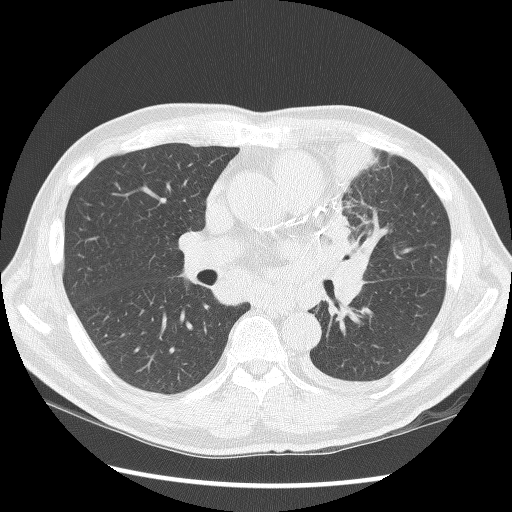
Axial slice from a low-dose chest CT screening exam; second annual screen; lung window (W 1500 / L -600 HU); 2.5 mm slice thickness; lung (sharp) reconstruction kernel (BONE); 120 kVp; slice 59 of 136 in the series; 512 × 512 image matrix. Male, age 64 years at enrolment. Former smoker at enrolment.
- Expert-annotated lung lesion, bounding box [x1, y1, x2, y2] px = [306, 130, 394, 278].
- No non-calcified nodule or mass ≥4 mm was recorded by the screening reader at this exam.
- Participant outcome: lung cancer diagnosed 24 days after this screen — small cell carcinoma, NOS, left upper lobe, stage IV (AJCC 6th edition), 100 mm at pathology.